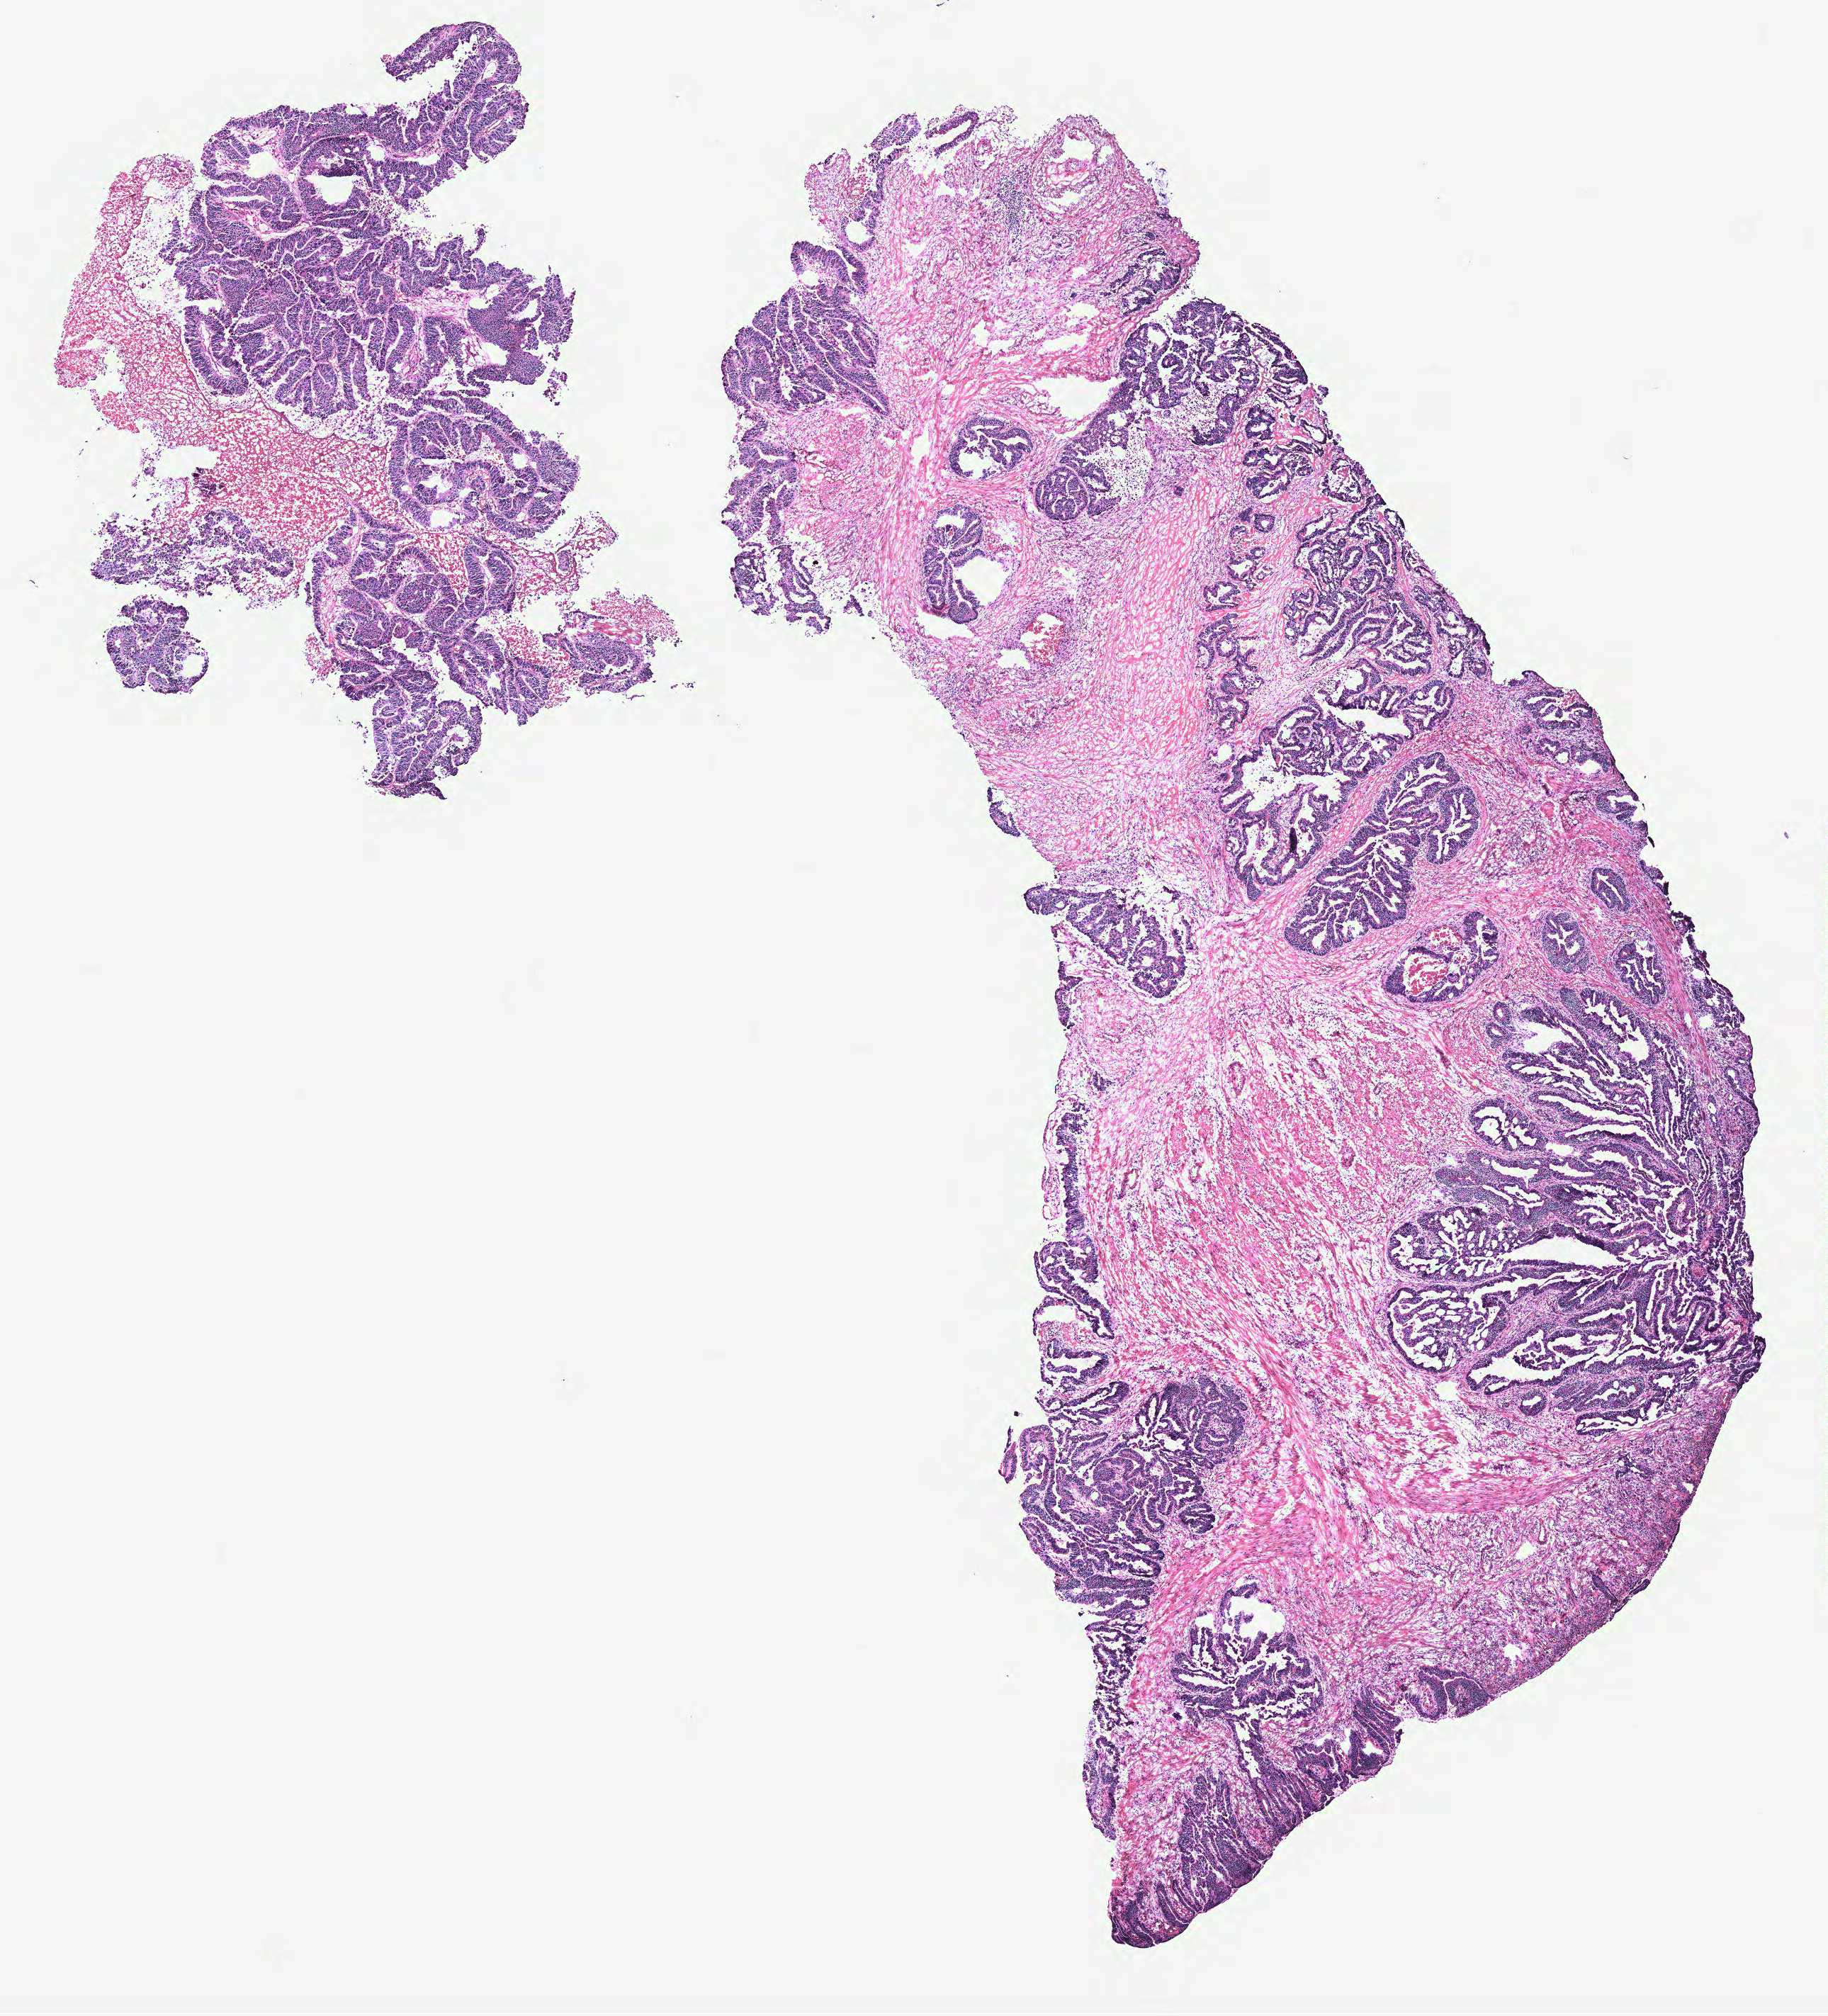
Digitized H&E-stained tissue section (whole slide) — shown as a low-resolution overview of the whole scanned area (about 10.3 x 11.4 mm); colon, tissue type not recorded.
* patient diagnosis (cohort enrolment): colon cancer (colon)